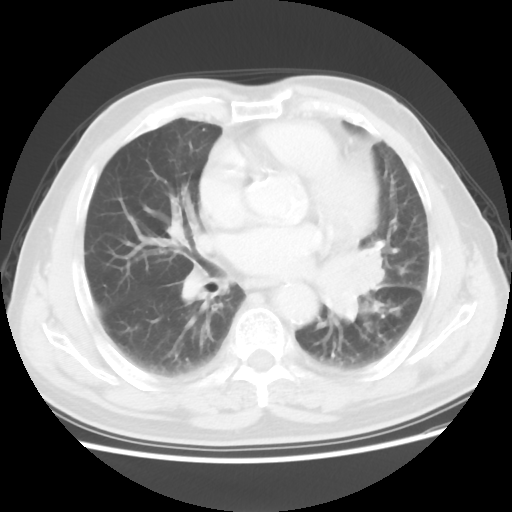
Chest CT, one axial slice. Position 29 of 56 along the scan axis. Reconstruction kernel STANDARD. Lung window (W 1500 / L -600 HU). 5 mm slice thickness. 512 × 512 image matrix, field of view 360 × 360 mm. Male patient, age 75 years. From the clinical record (not read from this slice): clinical TNM (as recorded): T3 N0 M0.
Annotated regions visible in this slice (bounding box drawn by a radiologist):
- lung tumour (recorded histology: squamous cell carcinoma): bounding box (x1, y1, x2, y2) in pixels: (316, 234, 392, 321)